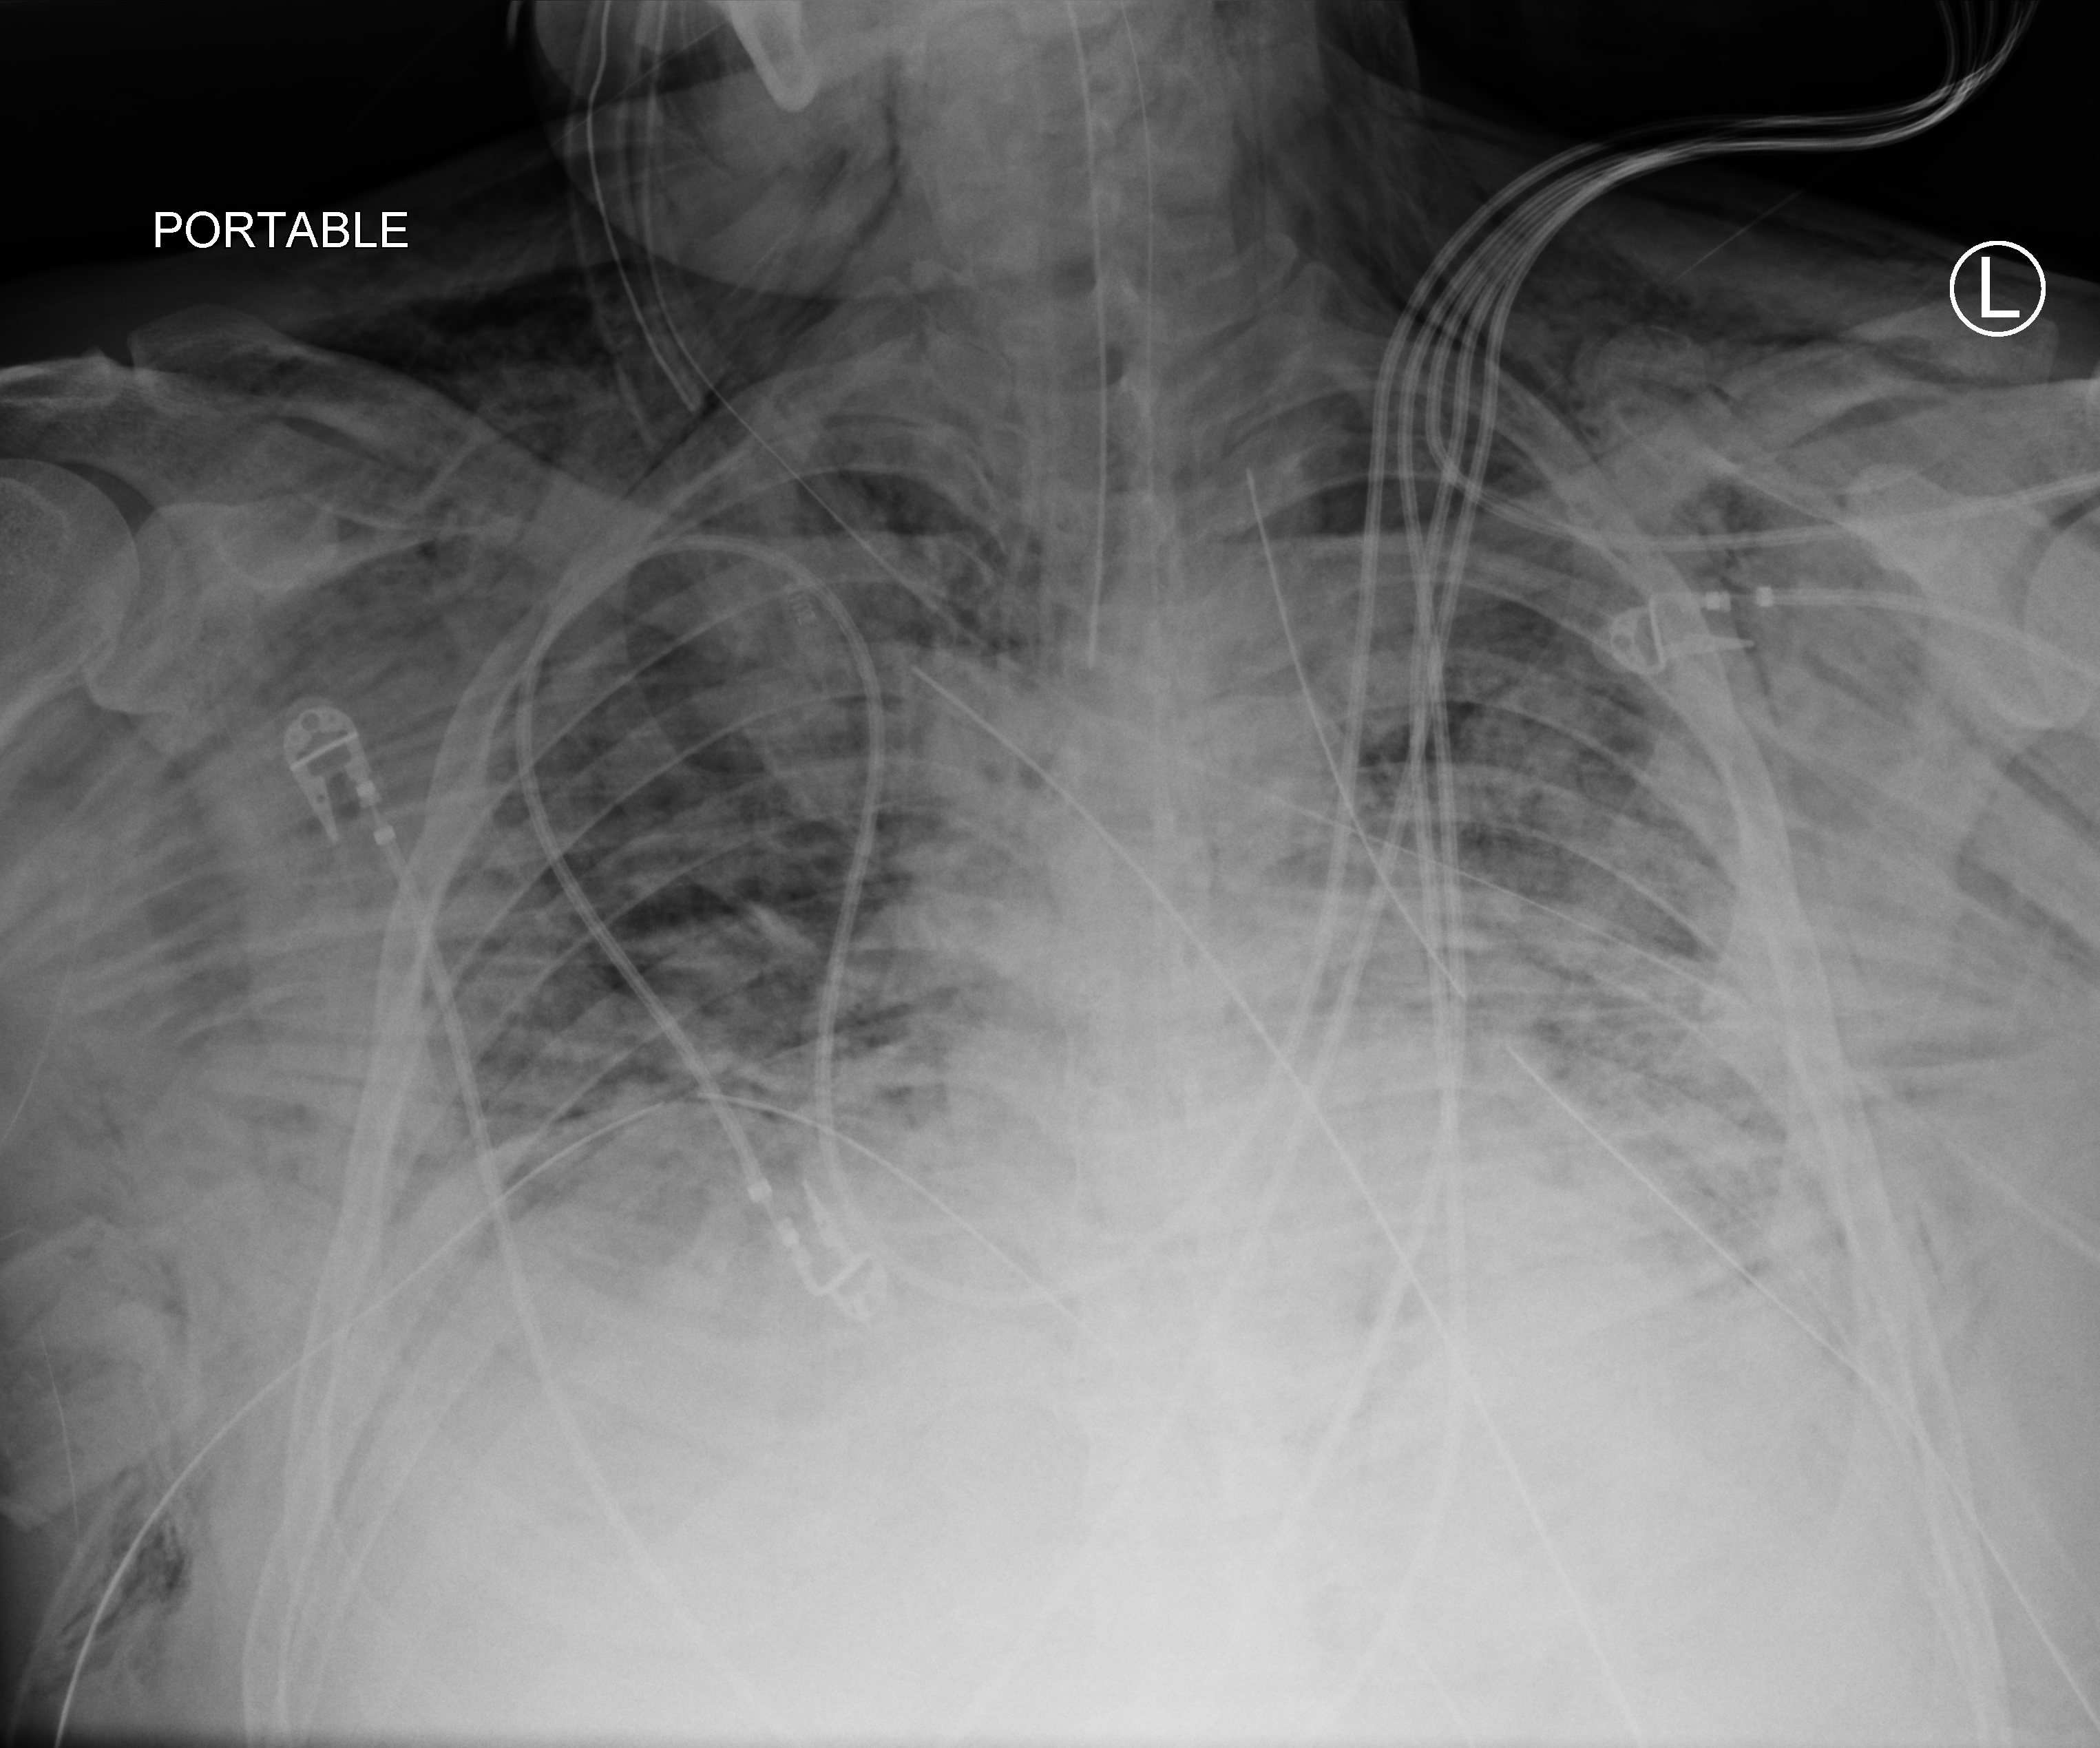
Chest X-ray (portable); anteroposterior (AP) projection. Male patient hospitalised with COVID-19, age 18–59 years.
From the hospital-stay record, not from the radiograph (when in the stay this image was taken is not recorded): admitted to intensive care during this hospital stay: yes; mechanically ventilated during this hospital stay: yes.